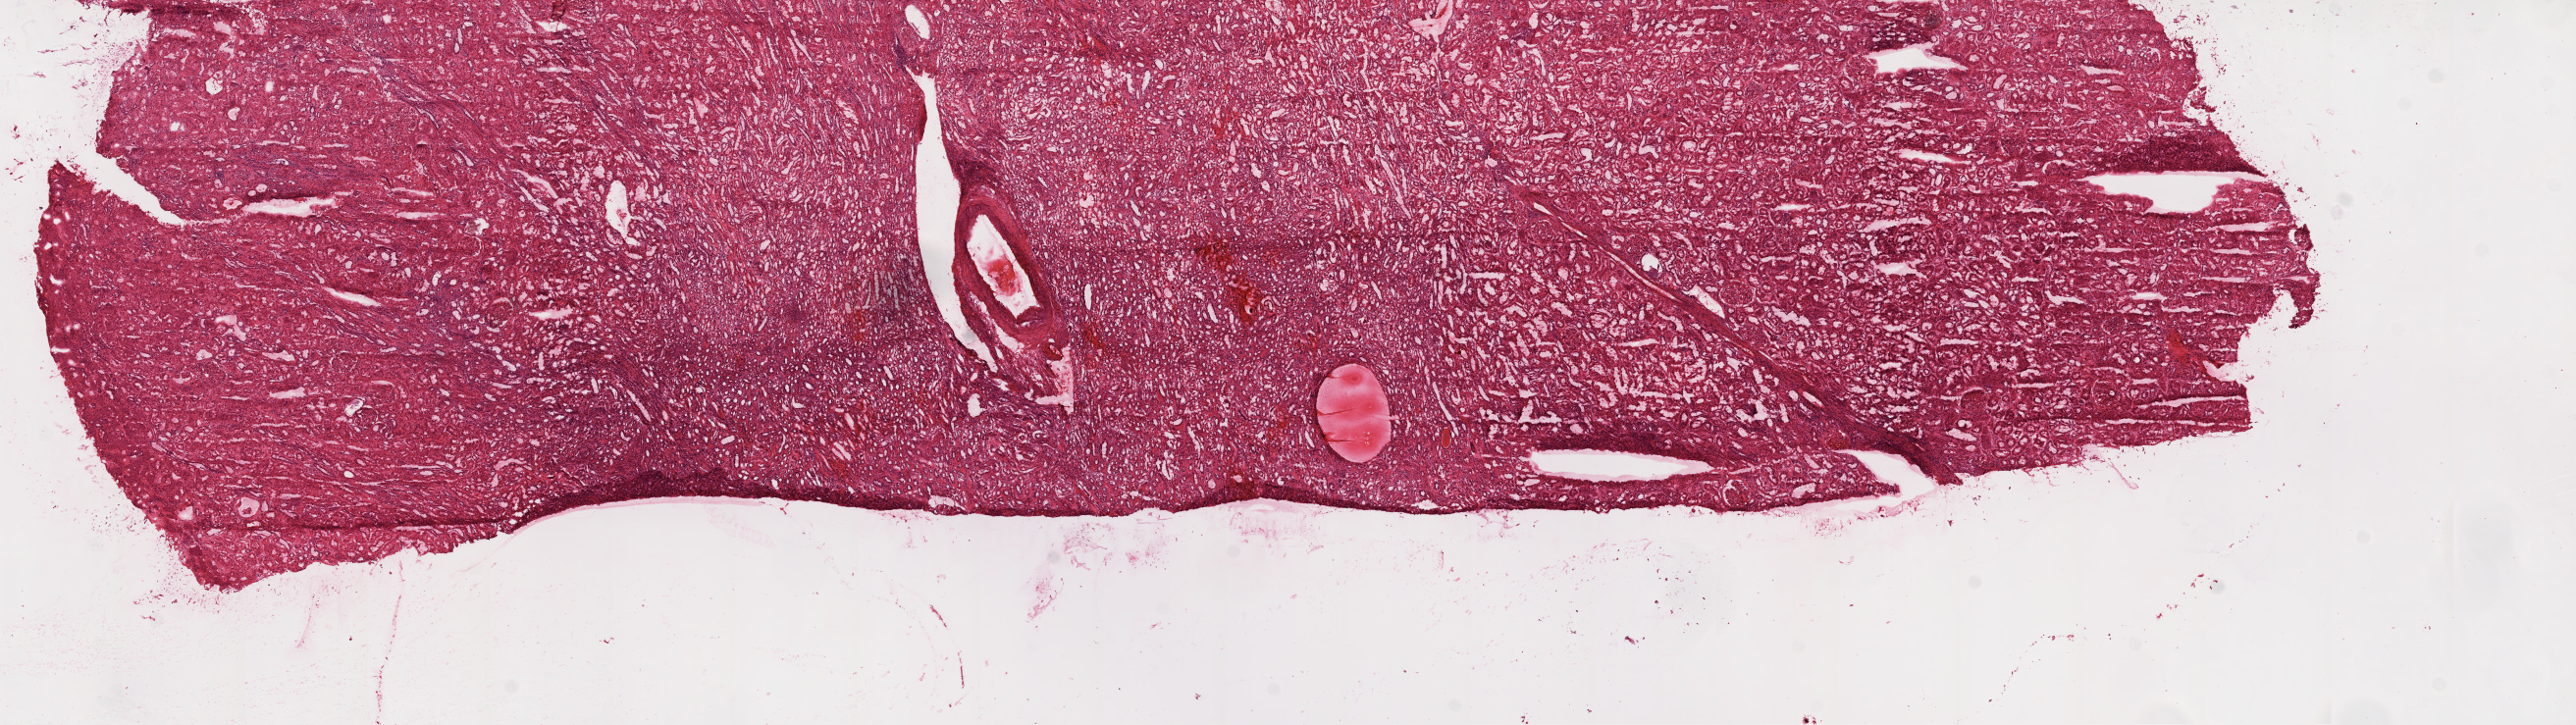
Whole-slide histology image, H&E, a low-resolution overview of the entire scanned area, about 21.1 x 5.9 mm (from a 20x scan). Frozen section from the top of the tissue portion. Sample: solid tissue normal (non-tumour tissue), kidney. Female patient; age at initial diagnosis 68 years.
This section: solid tissue normal (non-tumour) sample from the same patient. Patient diagnosis: Clear cell adenocarcinoma, NOS.